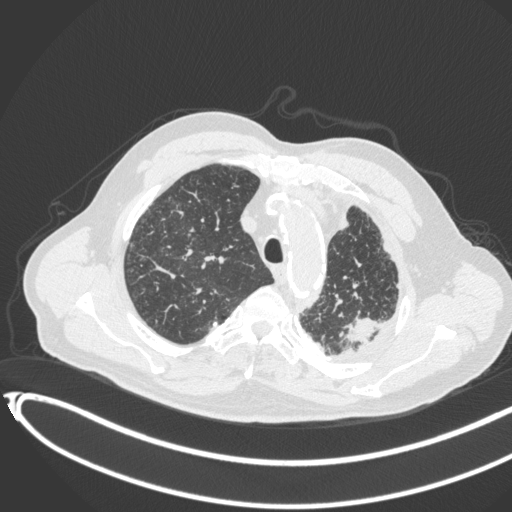
Chest CT, one axial slice. Position 341 of 451 along the scan axis. Reconstruction kernel B31f. 120 kVp. Lung window (W 1500 / L -600 HU). 512 × 512 image matrix, field of view 400 × 400 mm. Patient: male, 78 years. From the clinical record (not read from this slice): clinical TNM (as recorded): T1c N0 M1.
Annotated regions visible in this slice (bounding box drawn by a radiologist):
- lung tumour (recorded histology: adenocarcinoma): bounding box [x1, y1, x2, y2] px = [342, 312, 382, 343]